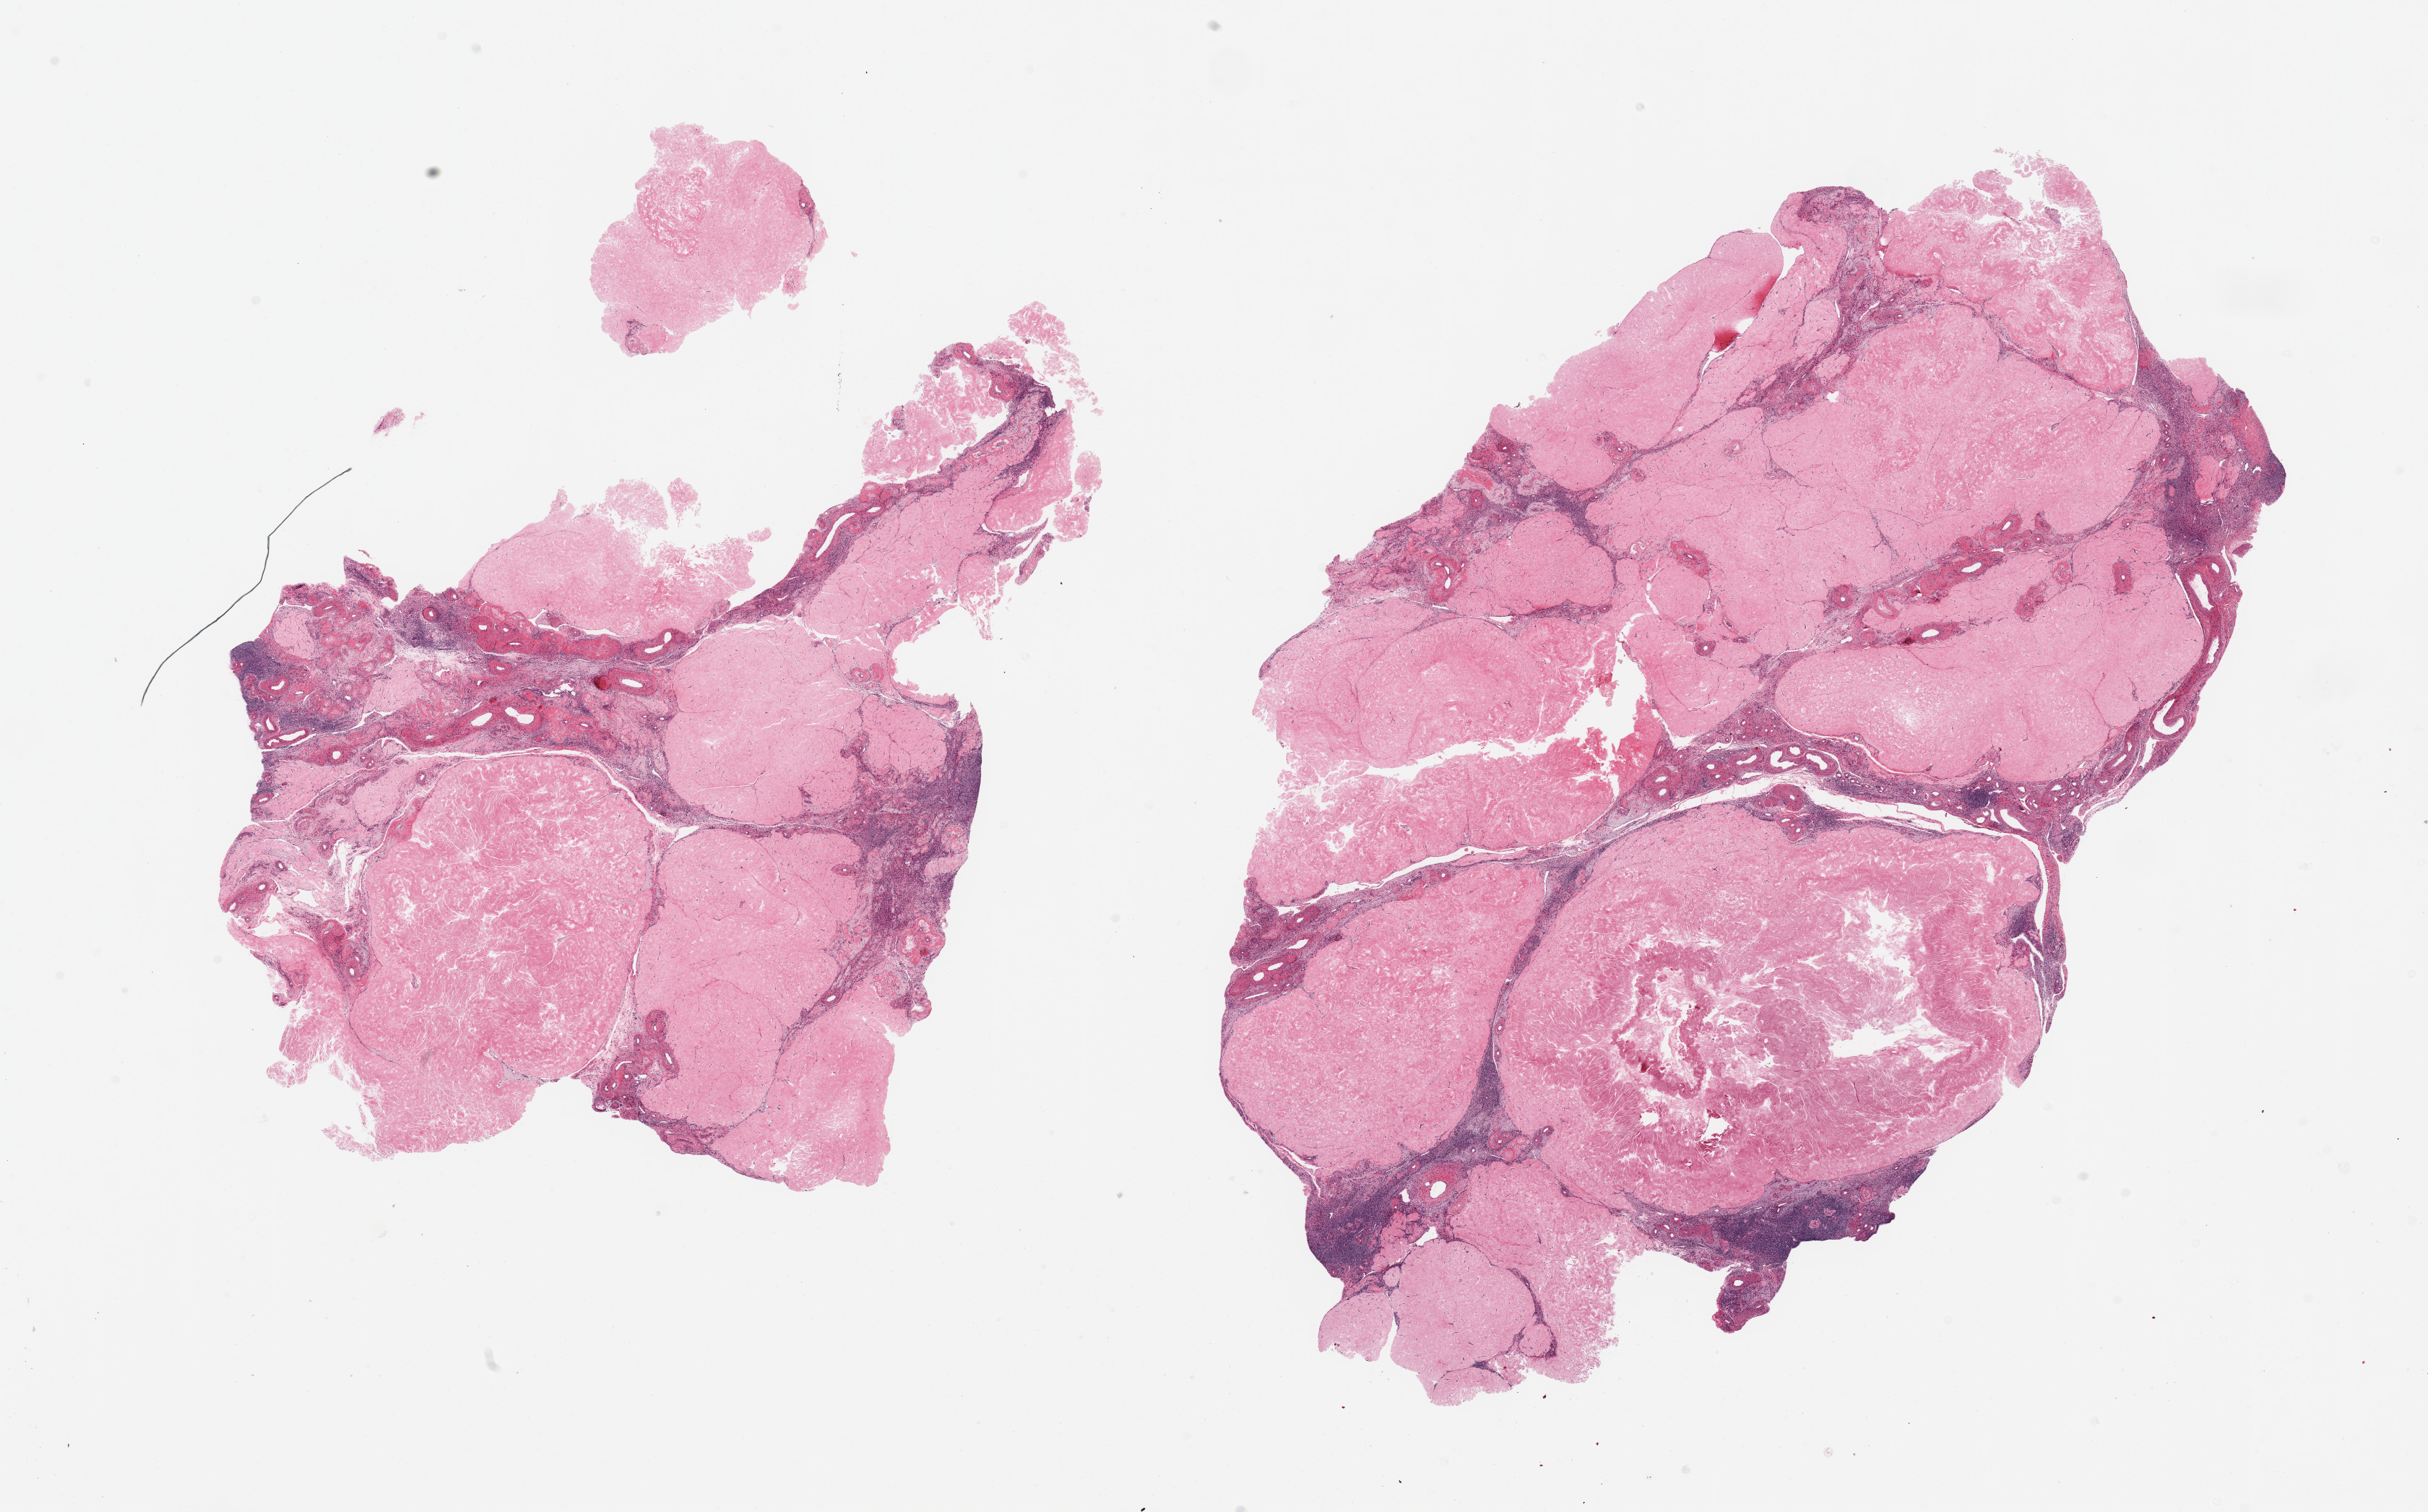
Digitized haematoxylin and eosin-stained section — low-resolution overview of the scanned area, about 26.6 x 16.6 mm. PAXgene-fixed, paraffin-embedded tissue. Sampled site (target tissue): ovary. Tissue donor sample.
• pathologist's review note for this sample: 2 pieces; corpora albicantia comprise 90% area